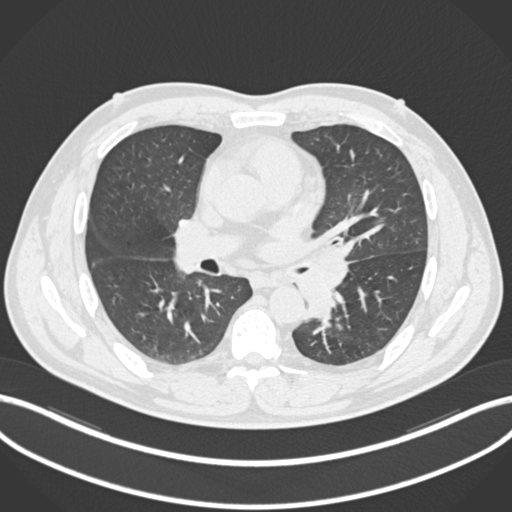
Chest CT, one axial slice. Position 122 of 223 along the scan axis. Lung window (W 1500 / L -600 HU). 1 mm slice thickness. 512 × 512 image matrix, field of view 400 × 400 mm. Patient: male, 50 years. From the clinical record (not read from this slice): clinical TNM (as recorded): T2a N3 M0.
Structures marked on this image (bounding box drawn by a radiologist):
- lung tumour (recorded histology: squamous cell carcinoma): box from (x=289, y=250) to (x=351, y=319) px